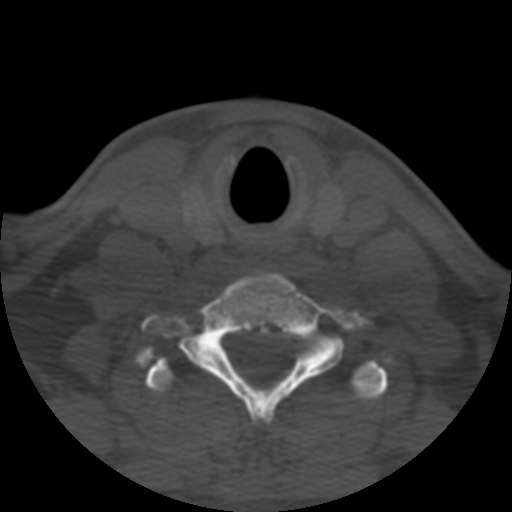
CT including the spine, one axial slice. Slice 461 of 508 in the series (ordered by position). Bone window (W 1800 / L 400 HU). 1.25 mm slice thickness. 512 × 512 image matrix, field of view 160 × 160 mm. Patient age 57 years. Case-level facts recorded for this patient, not image findings: primary cancer: prostate.
Annotated regions visible in this slice (semi-automatic segmentation, software-assisted and operator-edited):
- T1 vertebra: bounding box [x1, y1, x2, y2] px = [145, 358, 388, 400]